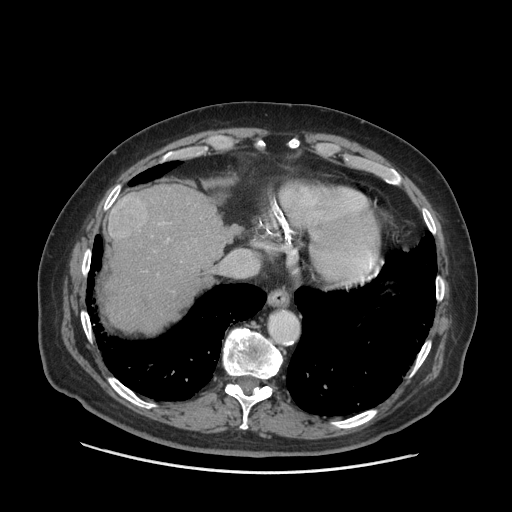
Contrast-enhanced abdominal CT (liver protocol), one axial slice; position 60 of 77 along the scan axis; reconstruction kernel STANDARD; 140 kVp; soft-tissue window (W 400 / L 40 HU); 2.5 mm slice thickness; 512 × 512 image matrix, field of view 420 × 420 mm. Case-level facts recorded for this patient, not image findings: diagnosis: hepatocellular carcinoma (patient treated with transarterial chemoembolisation; whether this scan precedes or follows treatment is not stated here); TNM stage (as recorded): Stage-I; Child-Pugh class: A; tumour differentiation: well differentiated; tumour nodularity: uninodular.
Annotated regions visible in this slice (semi-automatically segmented with operator editing):
- abdominal aorta: box from (x=270, y=312) to (x=299, y=341) px
- liver parenchyma outside the tumour (the mass and vessels are separate outlines, so this box may not span the whole liver): (x=104, y=184)–(x=234, y=332)
- mass: (x=108, y=194)–(x=149, y=241)